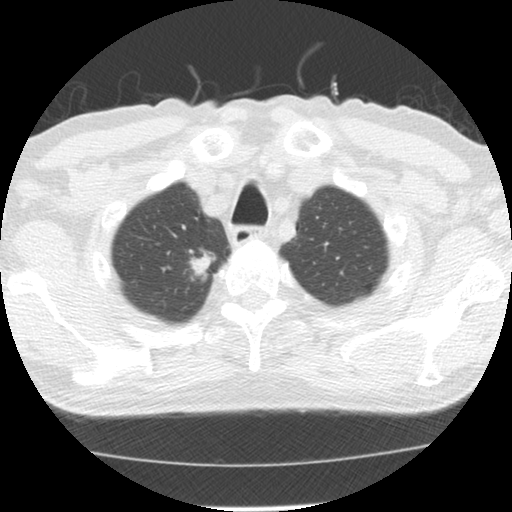
Axial slice from a low-dose chest CT screening exam, first (baseline) screen, lung window (W 1500 / L -600 HU), 2.5 mm slice thickness, 512 × 512 image matrix, field of view 310 × 310 mm. Male, age 64 years at enrolment. Former smoker at enrolment.
Expert-annotated lung lesion, bounding box [x1, y1, x2, y2] px = [179, 240, 224, 281]. Reader record for this screening exam (exam-level; its link to the box is not recorded): non-calcified nodule or mass ≥4 mm, right upper lobe, 20 × 13 mm, spiculated (stellate) margins, soft tissue attenuation. Later outcome: lung cancer diagnosed 73 days after this screen — adenocarcinoma, NOS, right upper lobe, moderately differentiated (G2), stage IA (AJCC 6th edition), 17 mm at pathology.